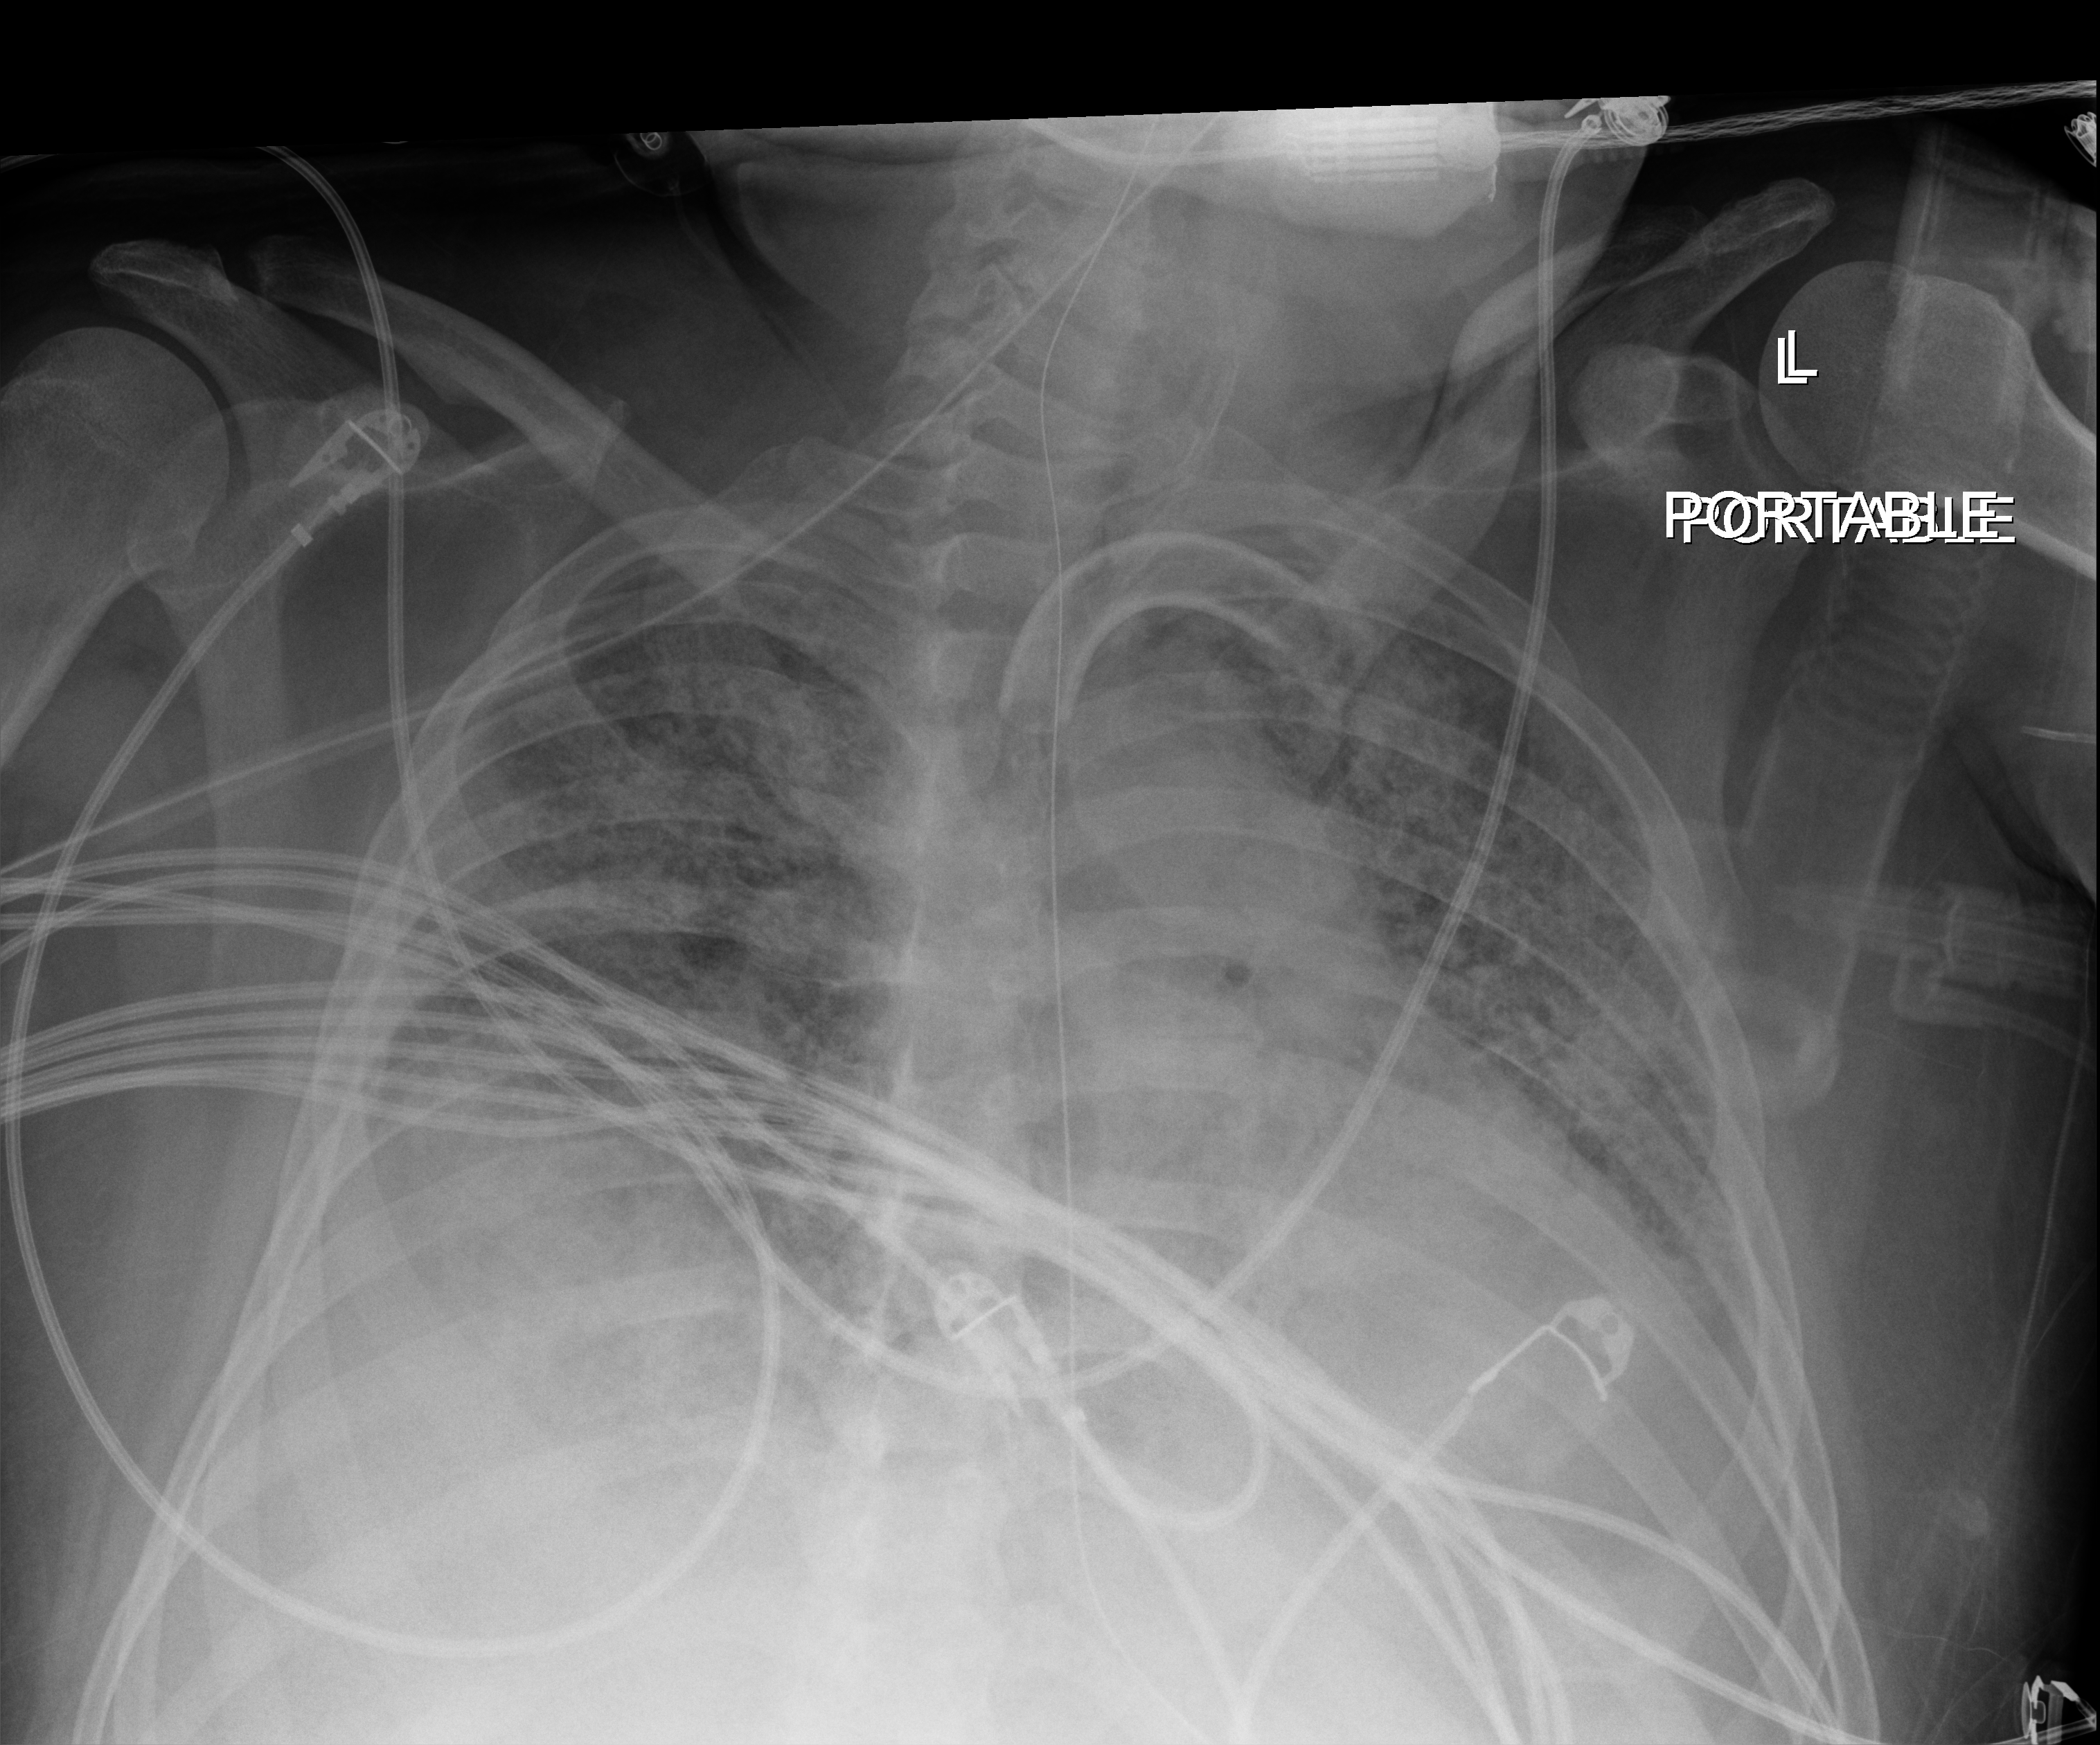
Portable chest radiograph, anteroposterior (AP) projection. Patient hospitalised with COVID-19; male, aged 18–59 years.
From the hospital-stay record, not from the radiograph (when in the stay this image was taken is not recorded): admitted to intensive care during this hospital stay: yes; chronic kidney disease (admission record): no.